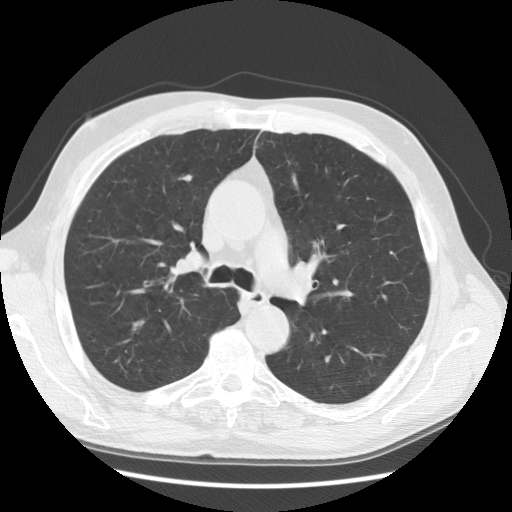
Low-dose screening chest CT, axial slice; baseline screening round; lung window (W 1500 / L -600 HU); 512 × 512 image matrix. Male participant, aged 60 years at enrolment. Current smoker at enrolment.
Expert reader's lesion annotation, box from (x=161, y=233) to (x=217, y=284) px. Screening reader's record for this exam: no non-calcified nodule ≥4 mm recorded. Official screen result: negative screen, minor abnormalities not suspicious for lung cancer. Participant outcome: lung cancer diagnosed 193 days after this screen — squamous cell carcinoma, NOS, right upper lobe, moderately differentiated (G2), stage IIIB (AJCC 6th edition), 52 mm at pathology.